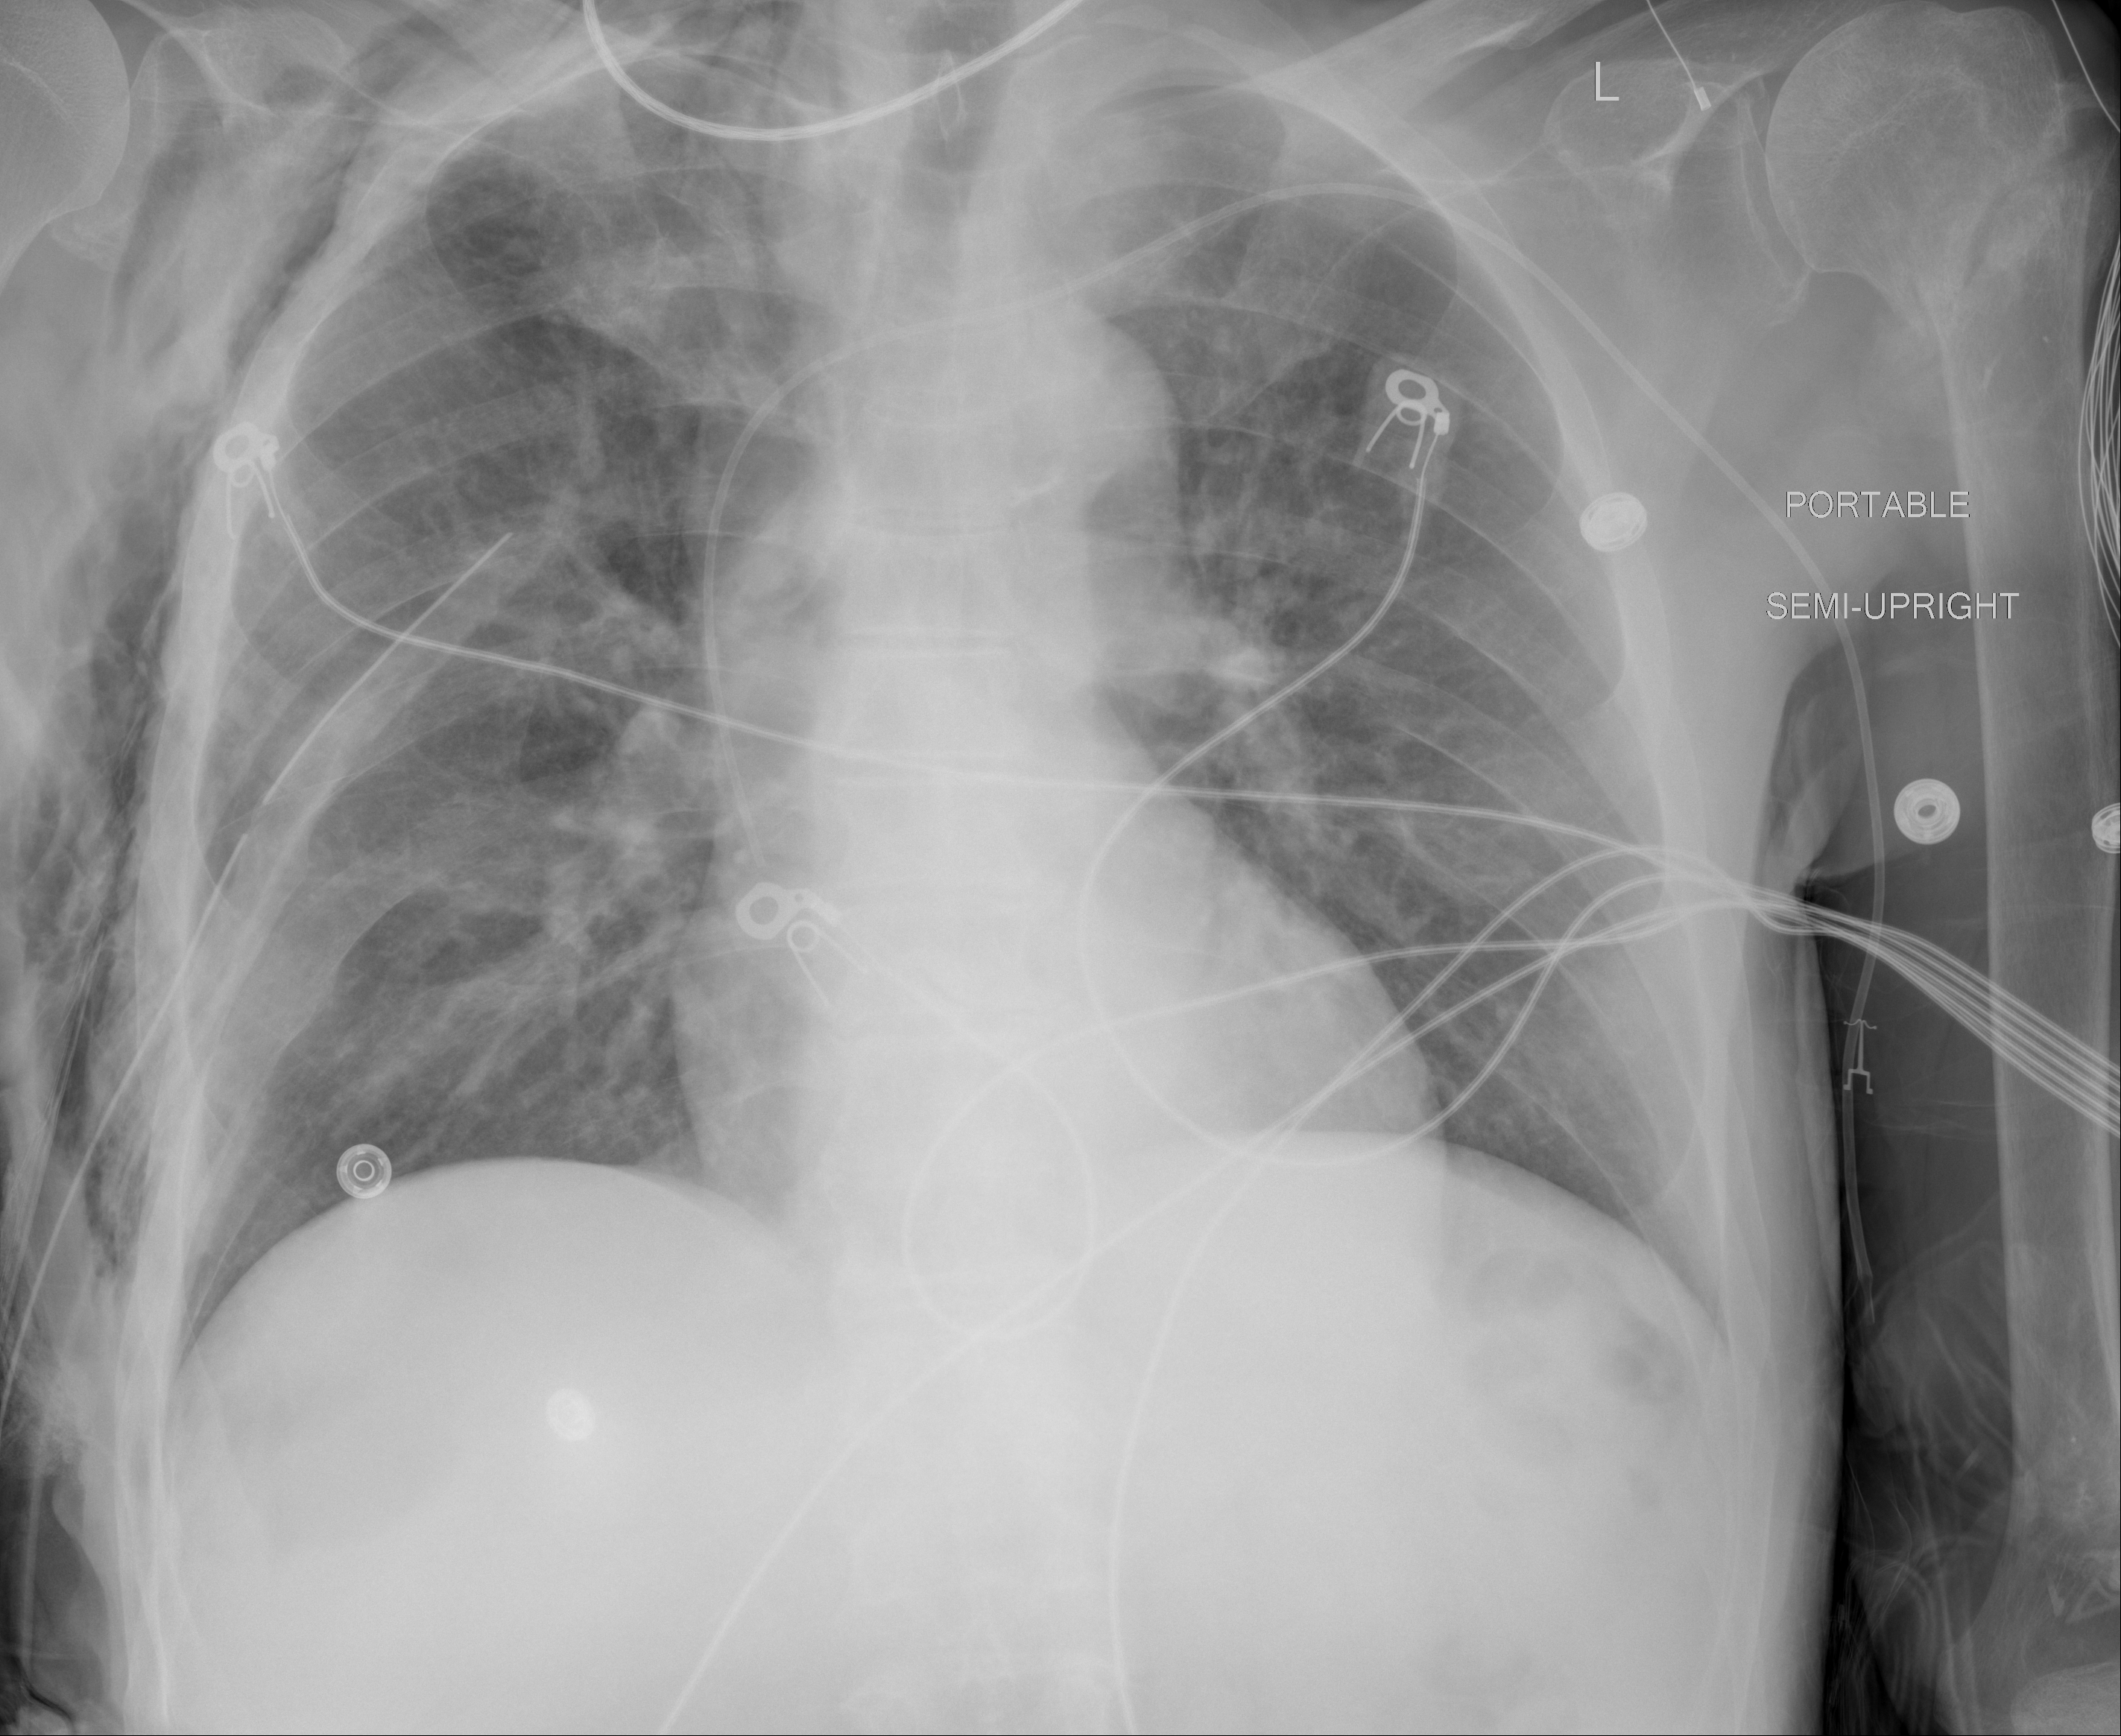
Chest X-ray (portable), AP projection. Male patient, age 59 years; imaged 4 days after the COVID-19 diagnosis.
Radiologist key findings (as recorded): Mild atelectatic changes at the right lung base. There is no focal consolidation. The left lung appears clear.